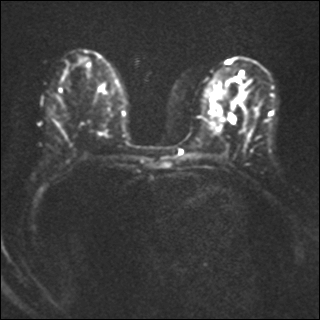
Breast MRI, one axial slice. Slice 20 of 40 in the series (ordered by position). Diffusion-weighted series; image 2 of 4 stored at this slice position (different b-values; order by instance number). 1.5 T. 4 mm slice thickness. 320 × 320 image matrix, field of view 320 × 320 mm. Female patient.
Annotated regions visible in this slice (manually delineated by an expert):
- tumour on diffusion-weighted imaging: bounding box (x1, y1, x2, y2) in pixels: (228, 115, 235, 123)